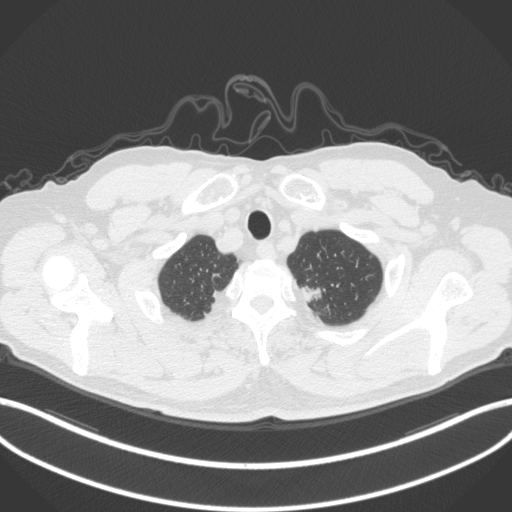
Chest CT, one axial slice. Position 350 of 382 along the scan axis. Reconstruction kernel B31f. Lung window (W 1500 / L -600 HU). 1 mm slice thickness. 512 × 512 image matrix. Male patient, age 64 years. Case-level facts recorded for this patient, not image findings: clinical TNM (as recorded): T1c N0 M0.
Structures marked on this image (rectangle marked by the reading radiologist):
- lung tumour (recorded histology: adenocarcinoma): box from (x=301, y=279) to (x=329, y=307) px